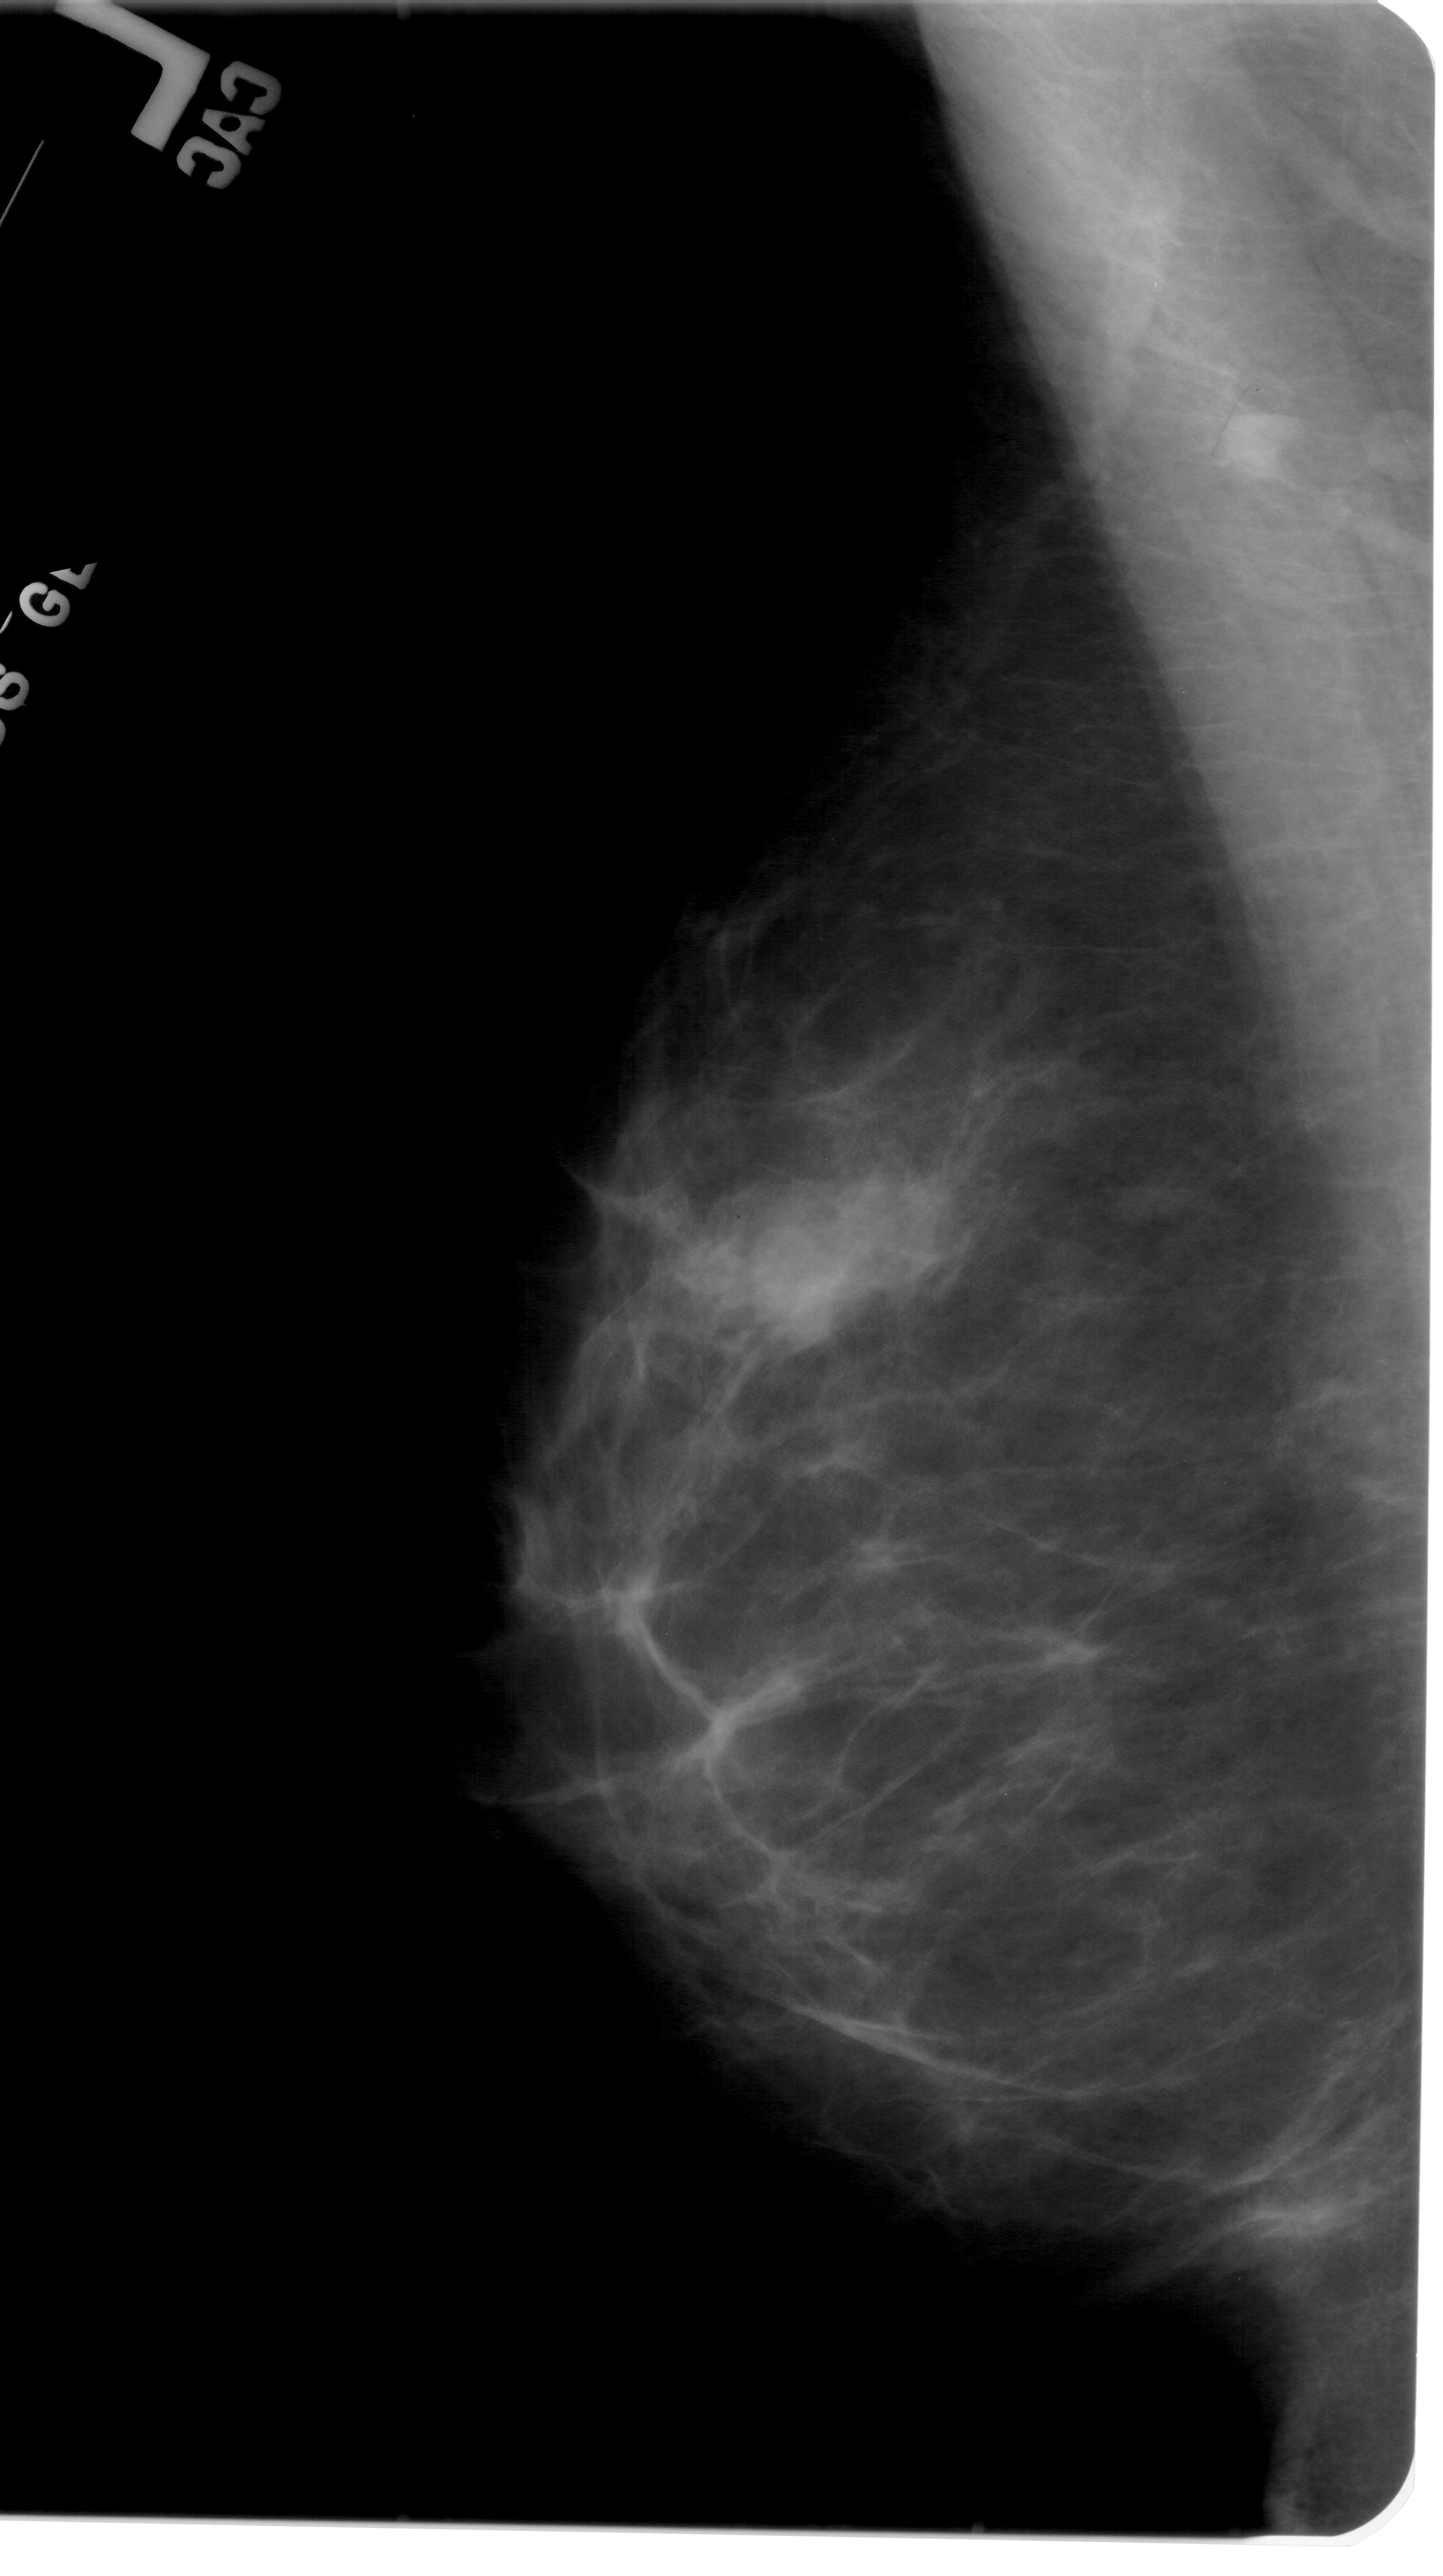
Digitized screen-film mammogram; left breast; mediolateral oblique (MLO) view; breast composition: almost entirely fatty (BI-RADS density category 1 of 4); 1443 × 2576 image matrix.
Expert-marked regions of interest on this image (one box per marked abnormality):
- mass, shape lobulated, margins obscured; BI-RADS assessment category 3; subtlety rating 3 on a 1 (subtle) to 5 (obvious) scale; pathology result (as recorded, not read from the image): benign: bounding box <748,1184,890,1331> (left, top, right, bottom; pixels)